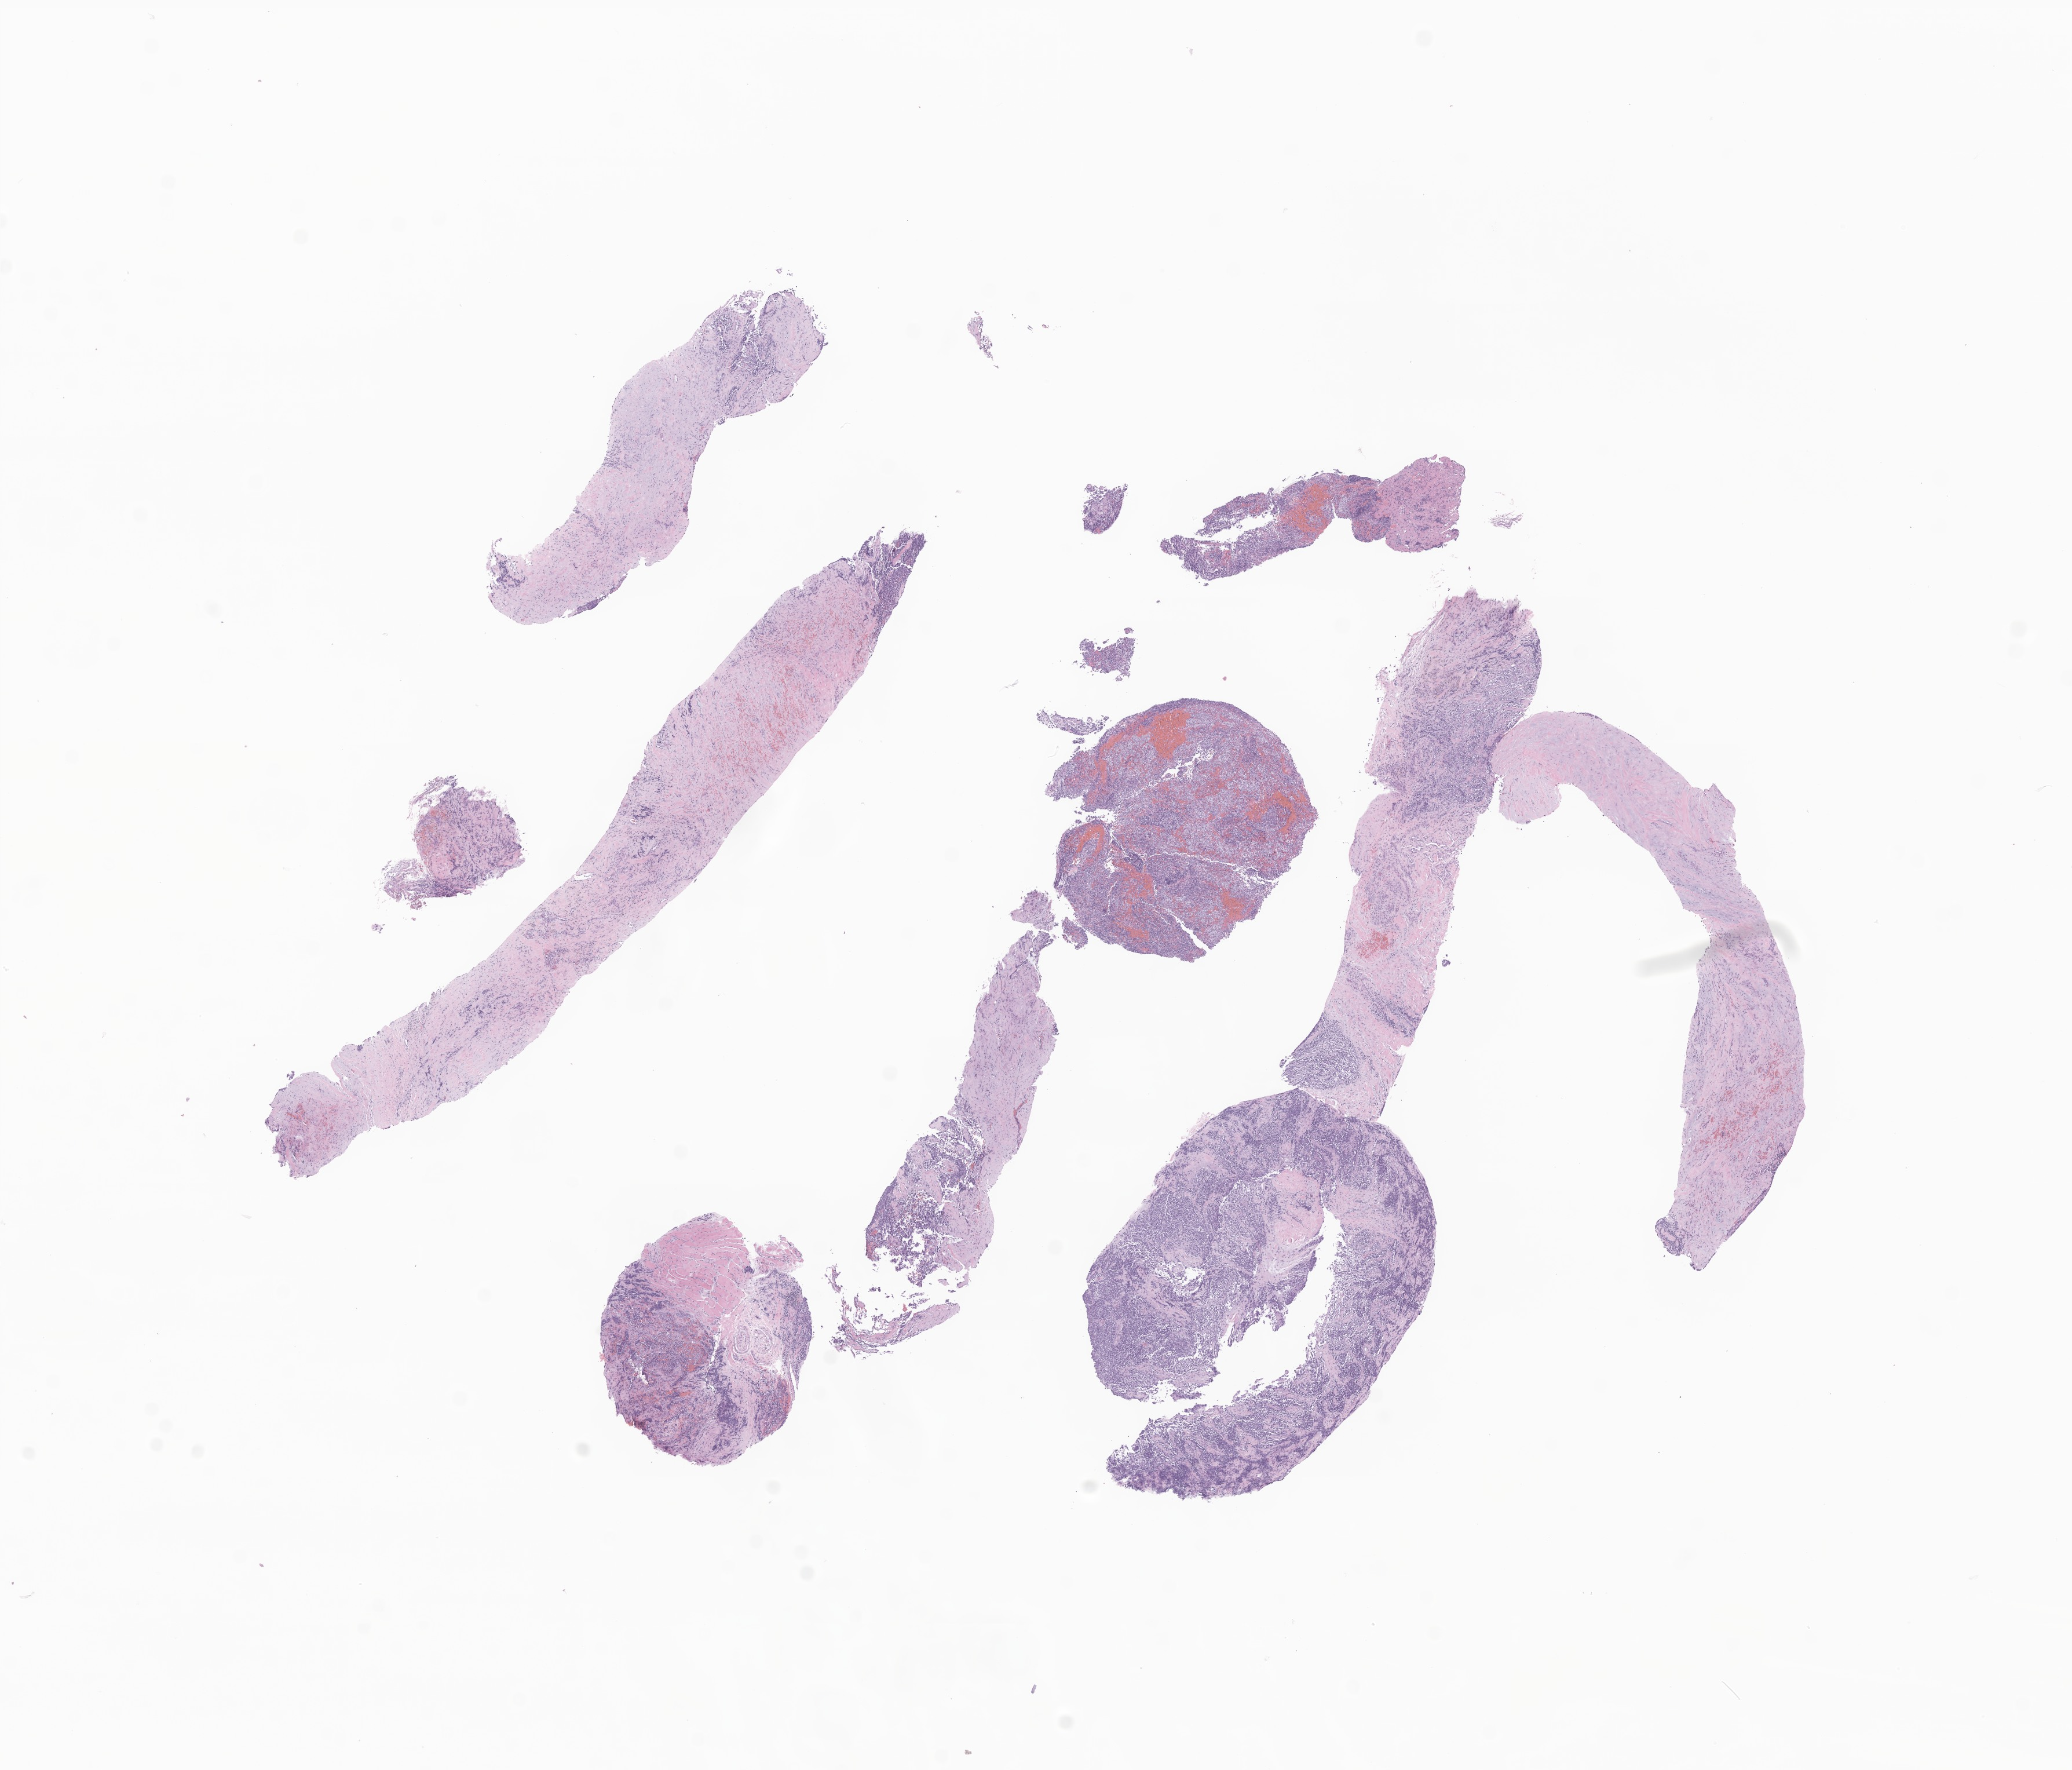
Digitized hematoxylin and eosin (H&E)-stained section of tumor tissue — low-resolution overview of the scanned area, about 15.1 x 12.9 mm. Formalin-fixed, paraffin-embedded (FFPE) tissue. Patient: male, age 161 months (13 years 5 months).
* diagnosis (ICD-O-3 morphology term): Neuroblastoma, NOS